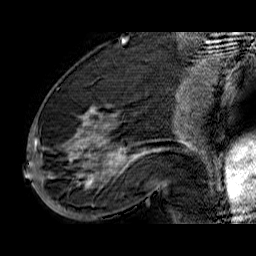
Breast MRI (dynamic contrast-enhanced), one sagittal slice. Slice 25 of 60 in the series (ordered by position). Dynamic contrast-enhanced series, time point 2 of 6 at this slice position (early post-contrast). 1.5 T. TE 6.5 ms, TR 32.9 ms. 4 mm slice thickness. 256 × 256 image matrix, field of view 200 × 200 mm. Female patient. Case-level facts recorded for this patient, not image findings: setting: breast cancer imaged before/during neoadjuvant chemotherapy; receptor status: HR-positive, HER2-negative.
Outlined on this slice (semi-automatically segmented with operator editing):
- analysis volume of interest (the breast-tissue region the enhancement analysis was run in; not a lesion): box from (x=33, y=74) to (x=176, y=210) px
- tumour enhancement mask (voxels above the 100 % enhancement threshold inside the analysis volume of interest): (x=33, y=109)–(x=146, y=187)